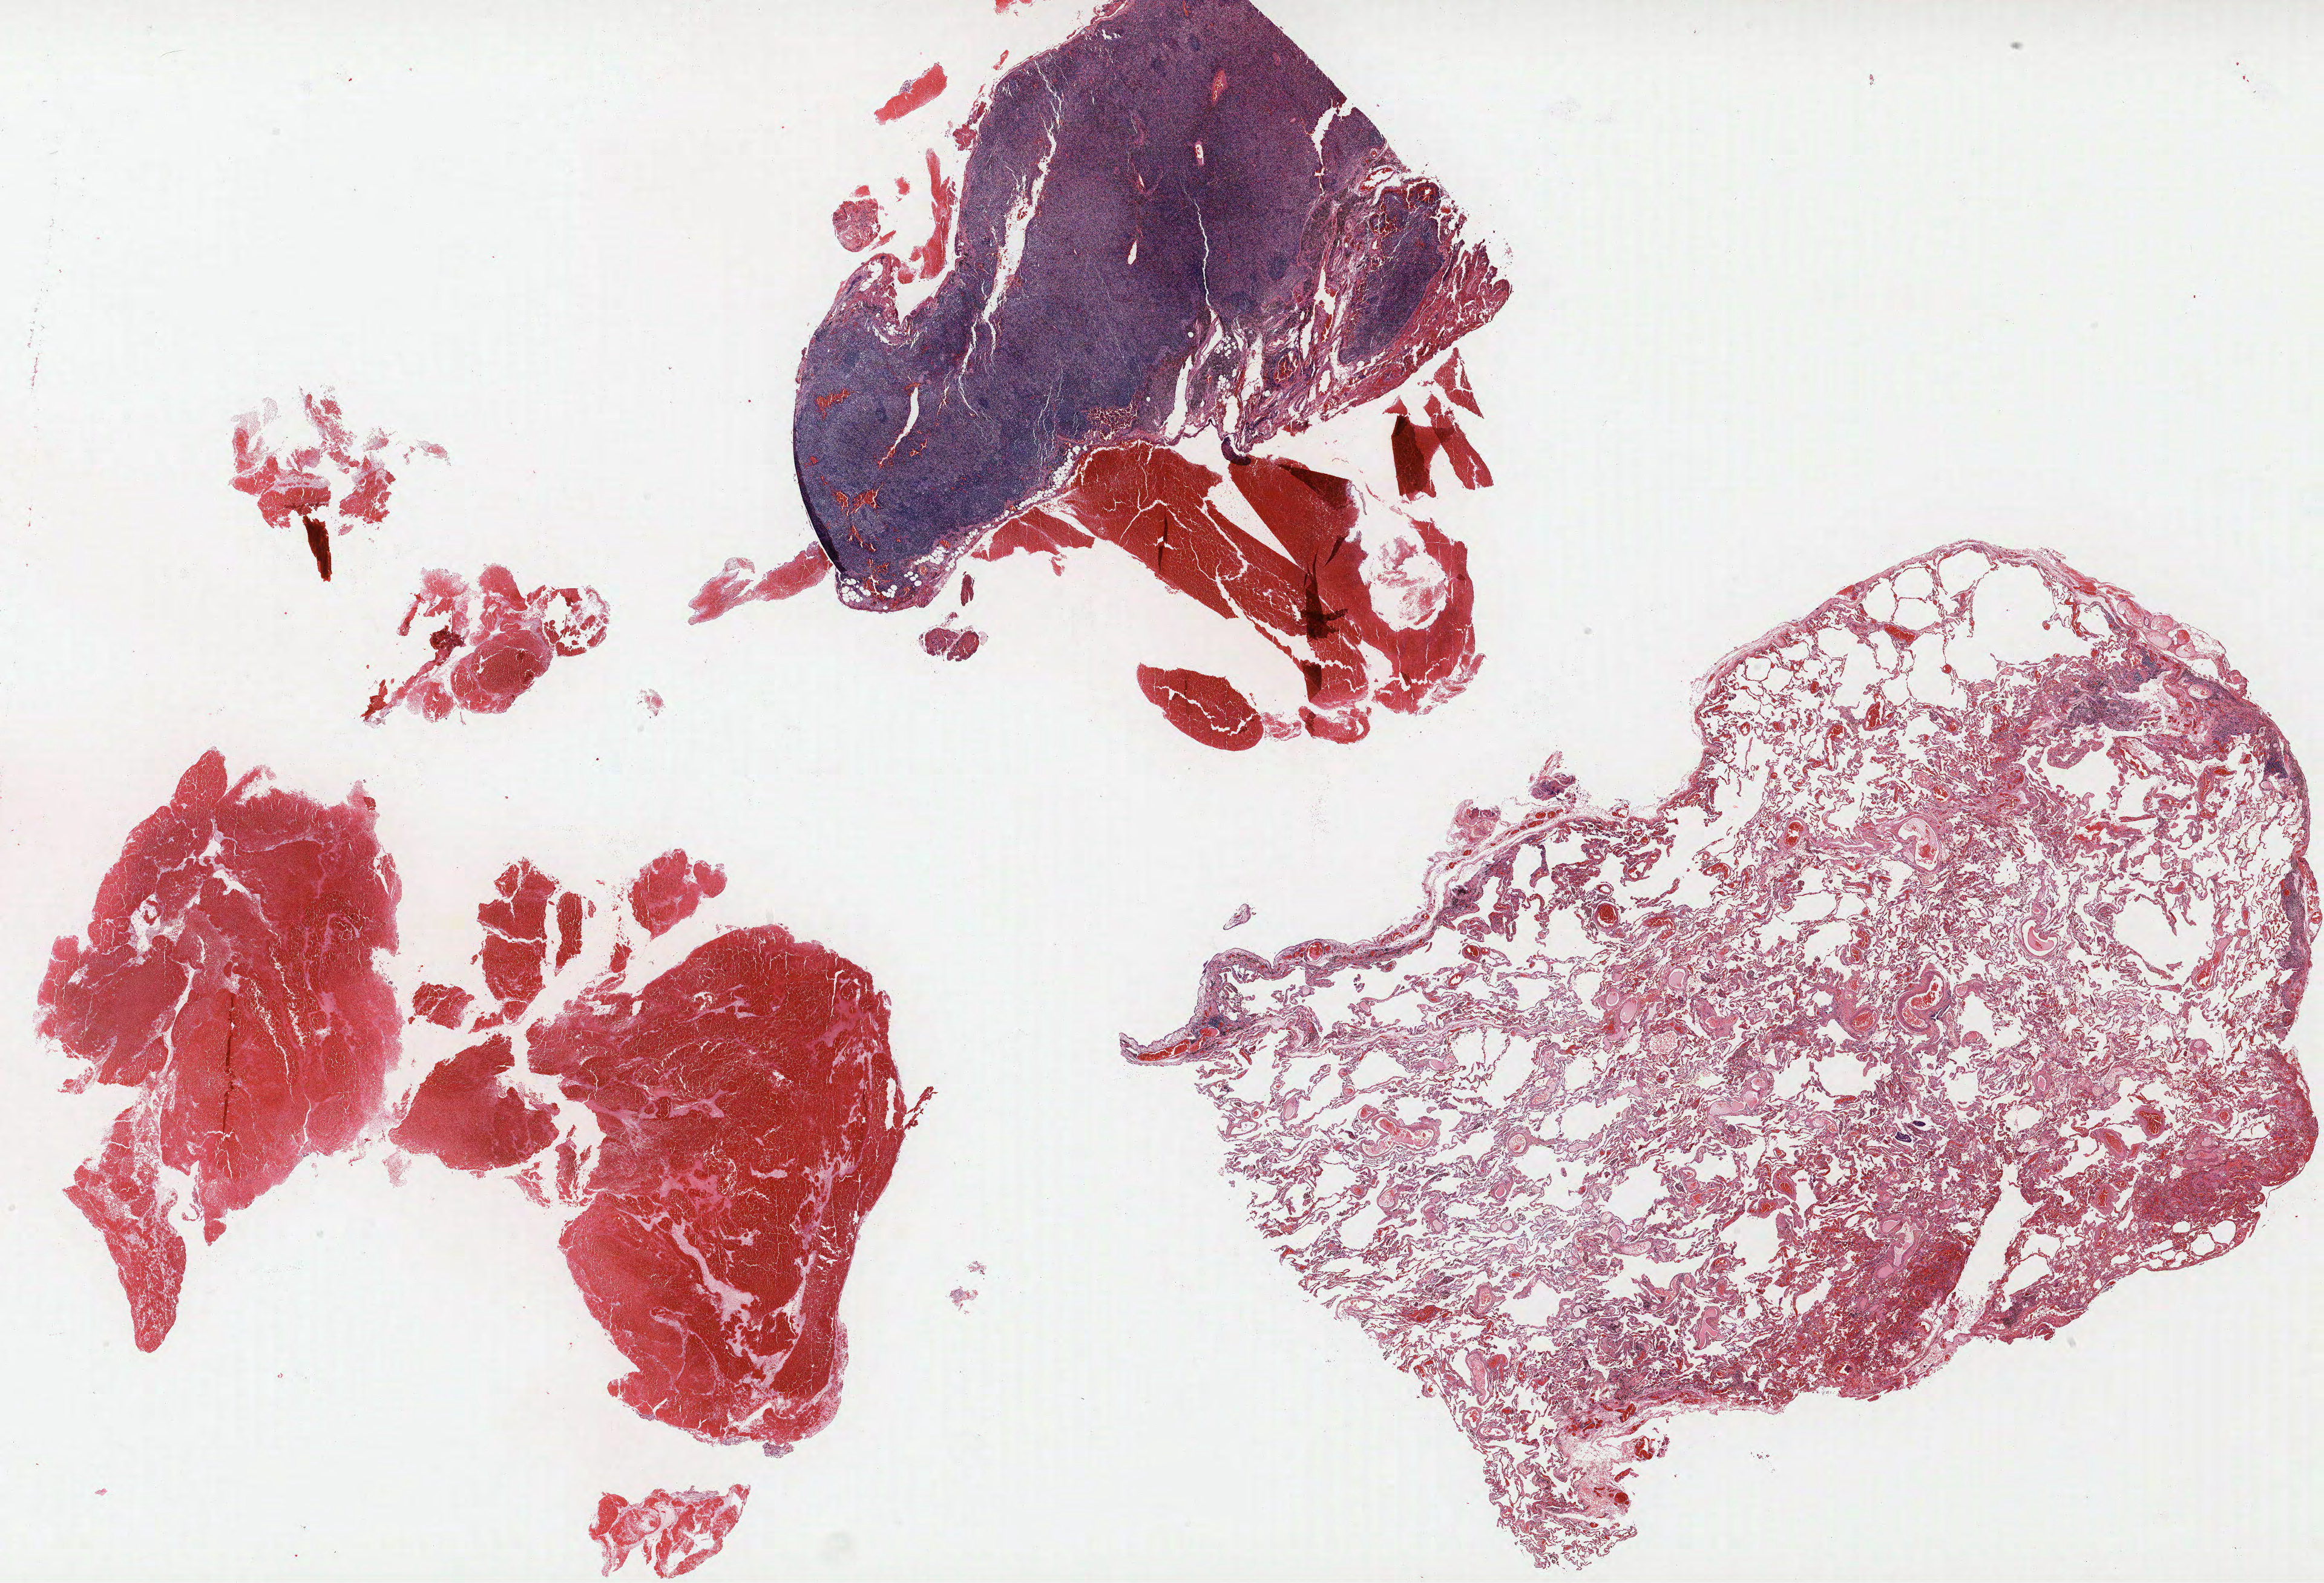
Whole-slide histology image, Hematoxylin and eosin (H&E) stained — whole scanned area (about 30.7 x 20.9 mm, from a 40x scan) shown as a low-resolution overview. Formalin-fixed paraffin-embedded (FFPE) section. Lung tissue. Male patient, aged 69 at enrolment. Current smoker at enrolment.
Participant's lung-cancer diagnosis: Squamous cell carcinoma, NOS.